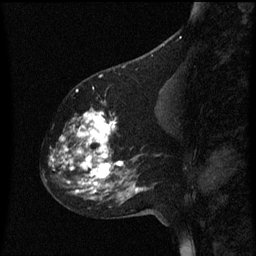
Breast MRI (dynamic contrast-enhanced), one sagittal slice. Position 26 of 60 along the scan axis. Dynamic contrast-enhanced series, image 2 of 3 at this slice position (ordered by acquisition). 1.5 T. TE 4.2 ms, TR 8 ms. 2 mm slice thickness. 256 × 256 image matrix, field of view 200 × 200 mm. Female patient, age 60 years.
Annotated regions visible in this slice (semi-automatically segmented with operator editing):
- analysis volume of interest (the breast-tissue region the enhancement analysis was run in; not a lesion): bounding box <49,108,158,197> (left, top, right, bottom; pixels)
- tumour enhancement mask (voxels above the 70 % enhancement threshold inside the analysis volume of interest): <50,108,139,195>